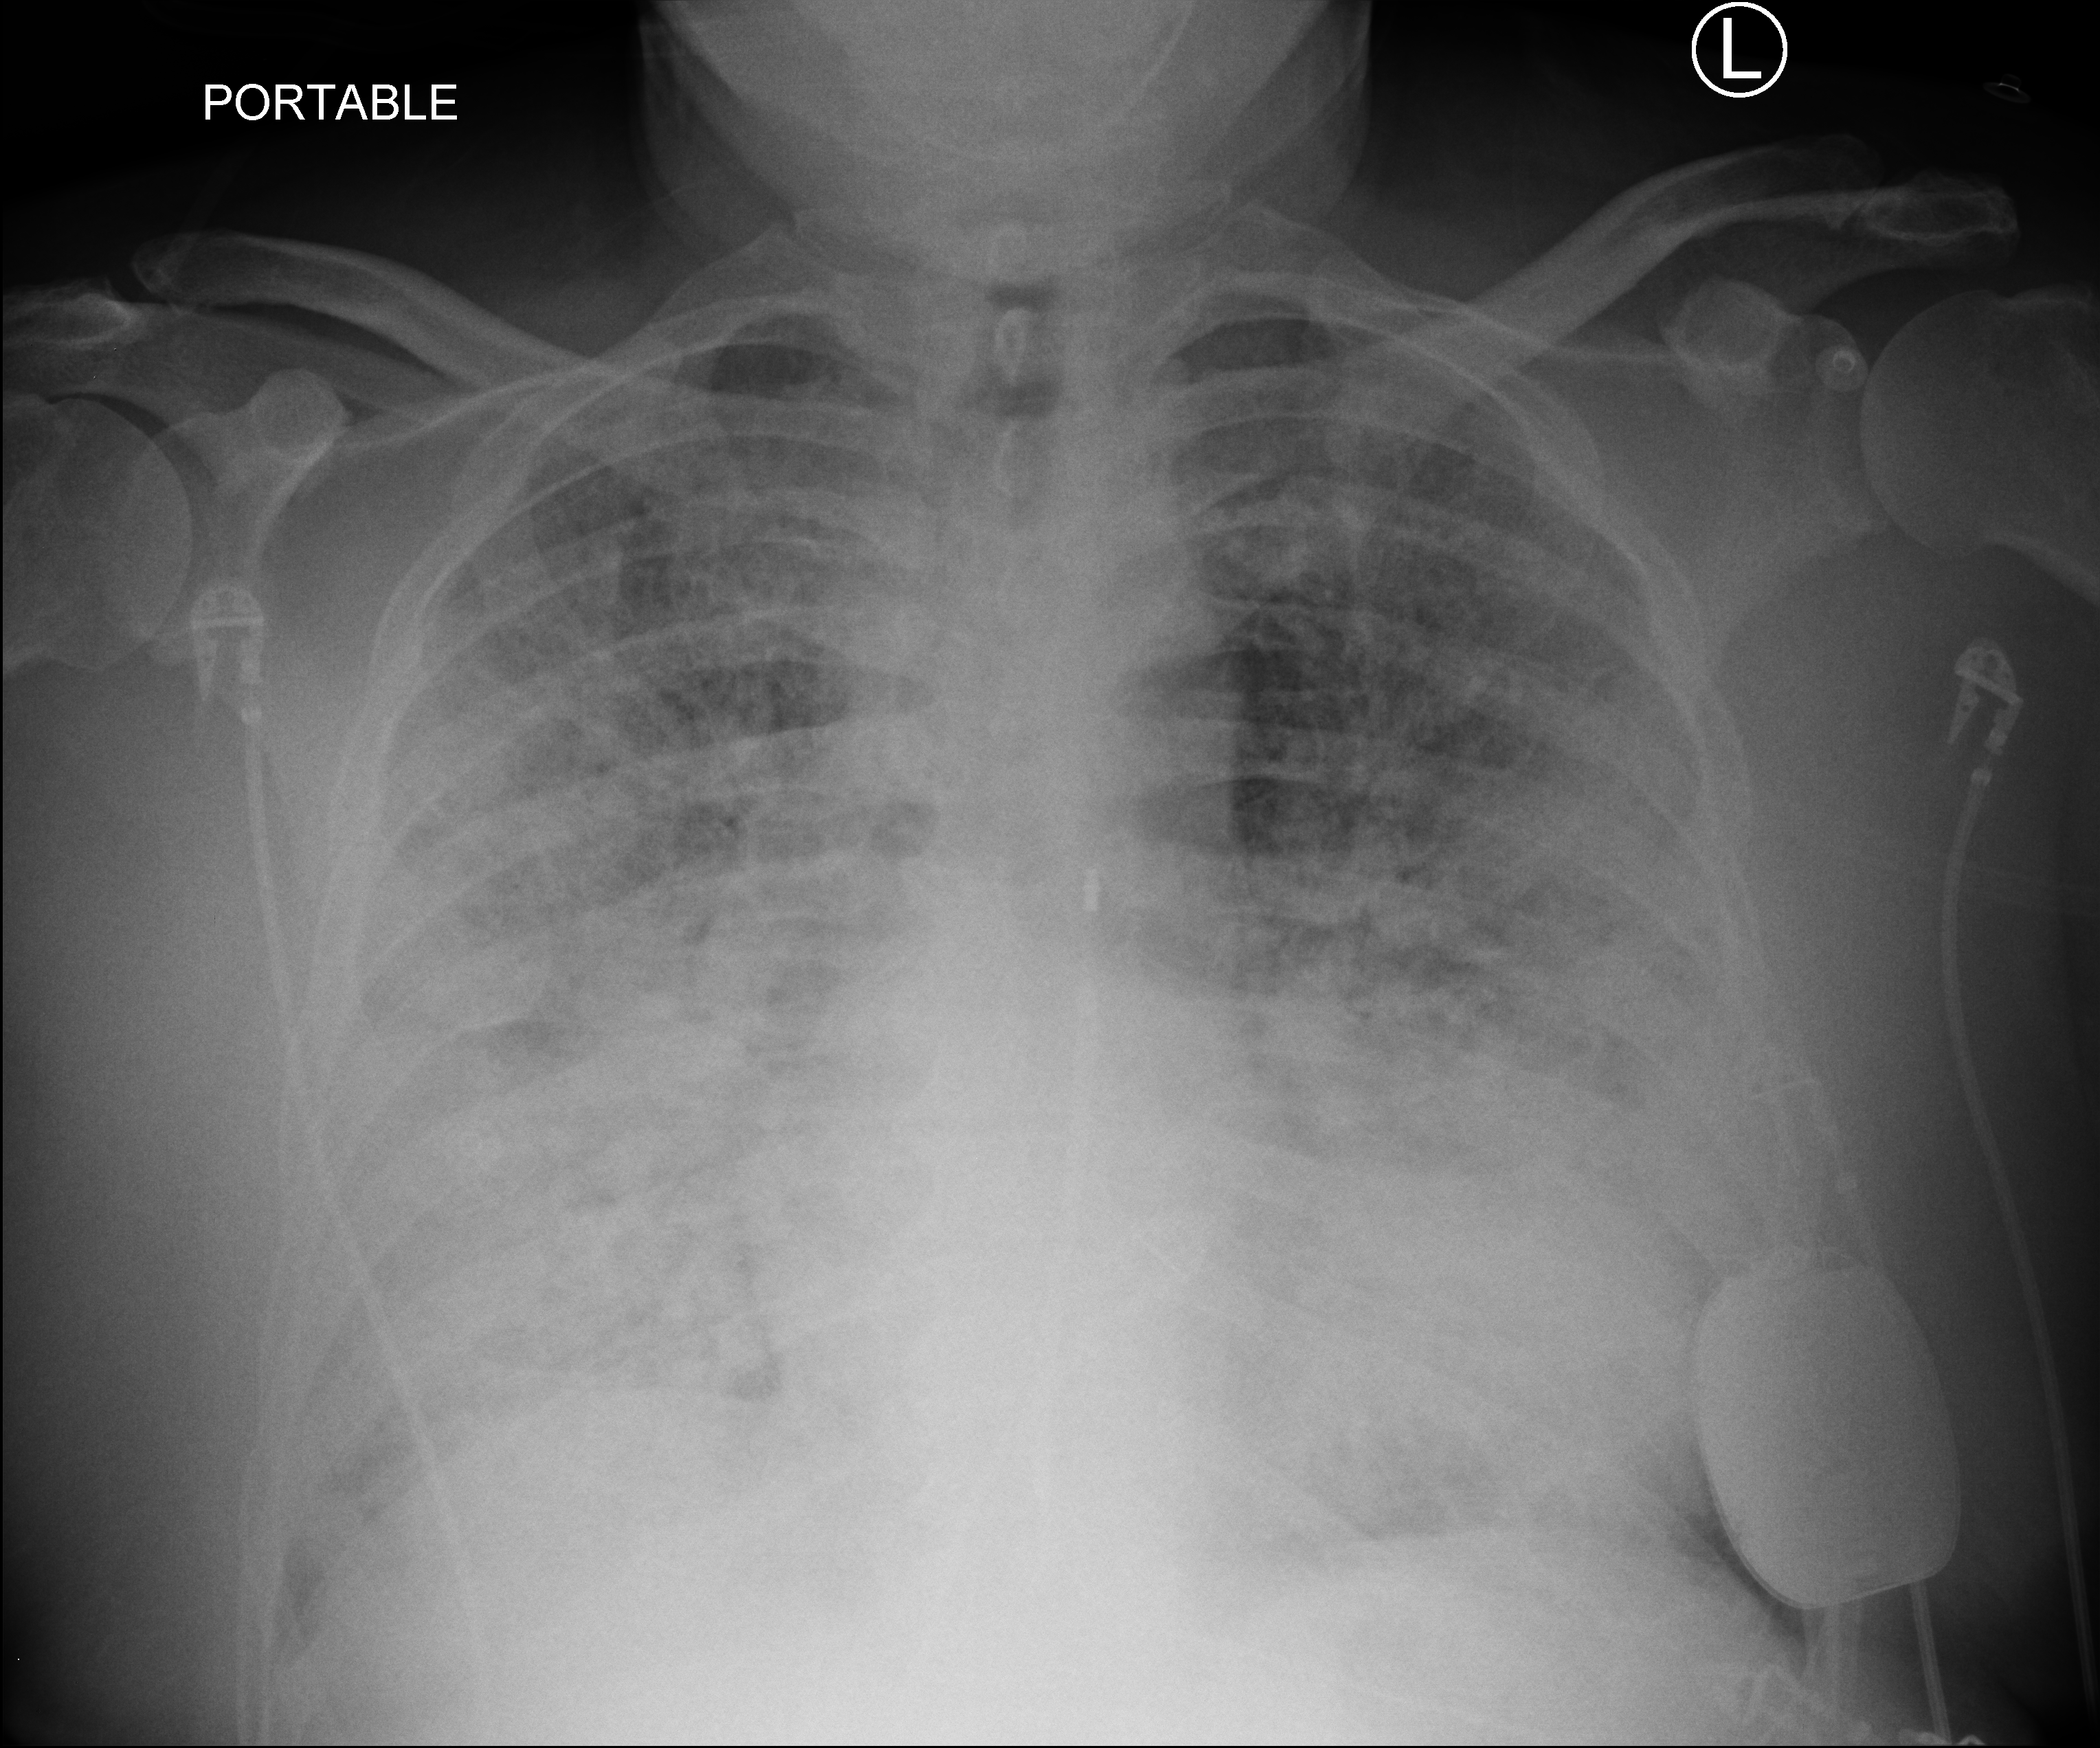
Portable chest radiograph, anteroposterior (AP) projection. Male patient hospitalised with COVID-19, age 60–74 years.
Admission-level facts for this patient (not findings on this image; timing relative to this image not recorded): smoking status (admission record): never; mechanically ventilated during this hospital stay: yes; admitted to intensive care during this hospital stay: yes.